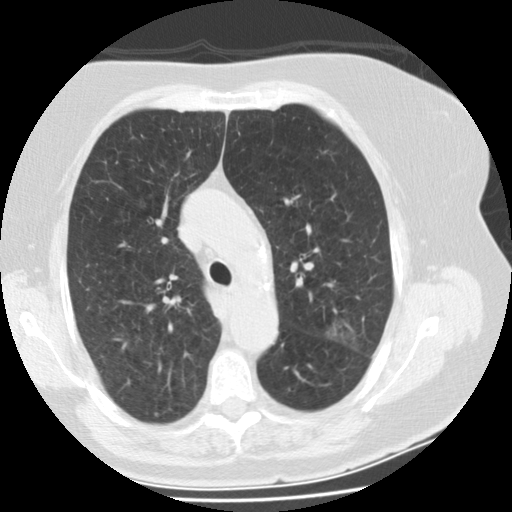
Low-dose screening chest CT, one axial slice. Slice 108 of 151 in the series (ordered by position). Reconstruction kernel STANDARD. 120 kVp. One of 2 acquisitions stored at this slice position. Lung window (W 1500 / L -600 HU). 512 × 512 image matrix, field of view 321 × 321 mm.
Outlined on this slice (outlined manually by an expert reader):
- lesion 1 (tumor, upper lobe of left lung): bounding box (x1, y1, x2, y2) in pixels: (327, 320, 360, 348)